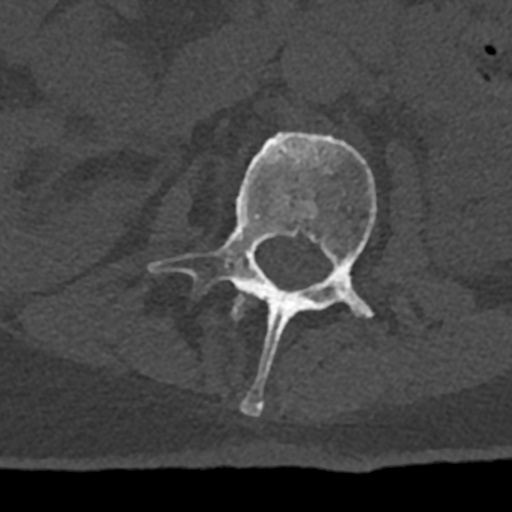
CT including the spine, one axial slice; slice 379 of 797 in the series (ordered by position); bone window (W 1800 / L 400 HU); 0.5 mm slice thickness; 512 × 512 image matrix, field of view 160 × 160 mm. Male patient, age 74 years. From the clinical record (not read from this slice): primary cancer: renal.
Annotated regions visible in this slice (semi-automatic segmentation, software-assisted and operator-edited):
- L1 vertebra: bounding box <233,298,246,319> (left, top, right, bottom; pixels)
- L2 vertebra: <148,132,377,417>